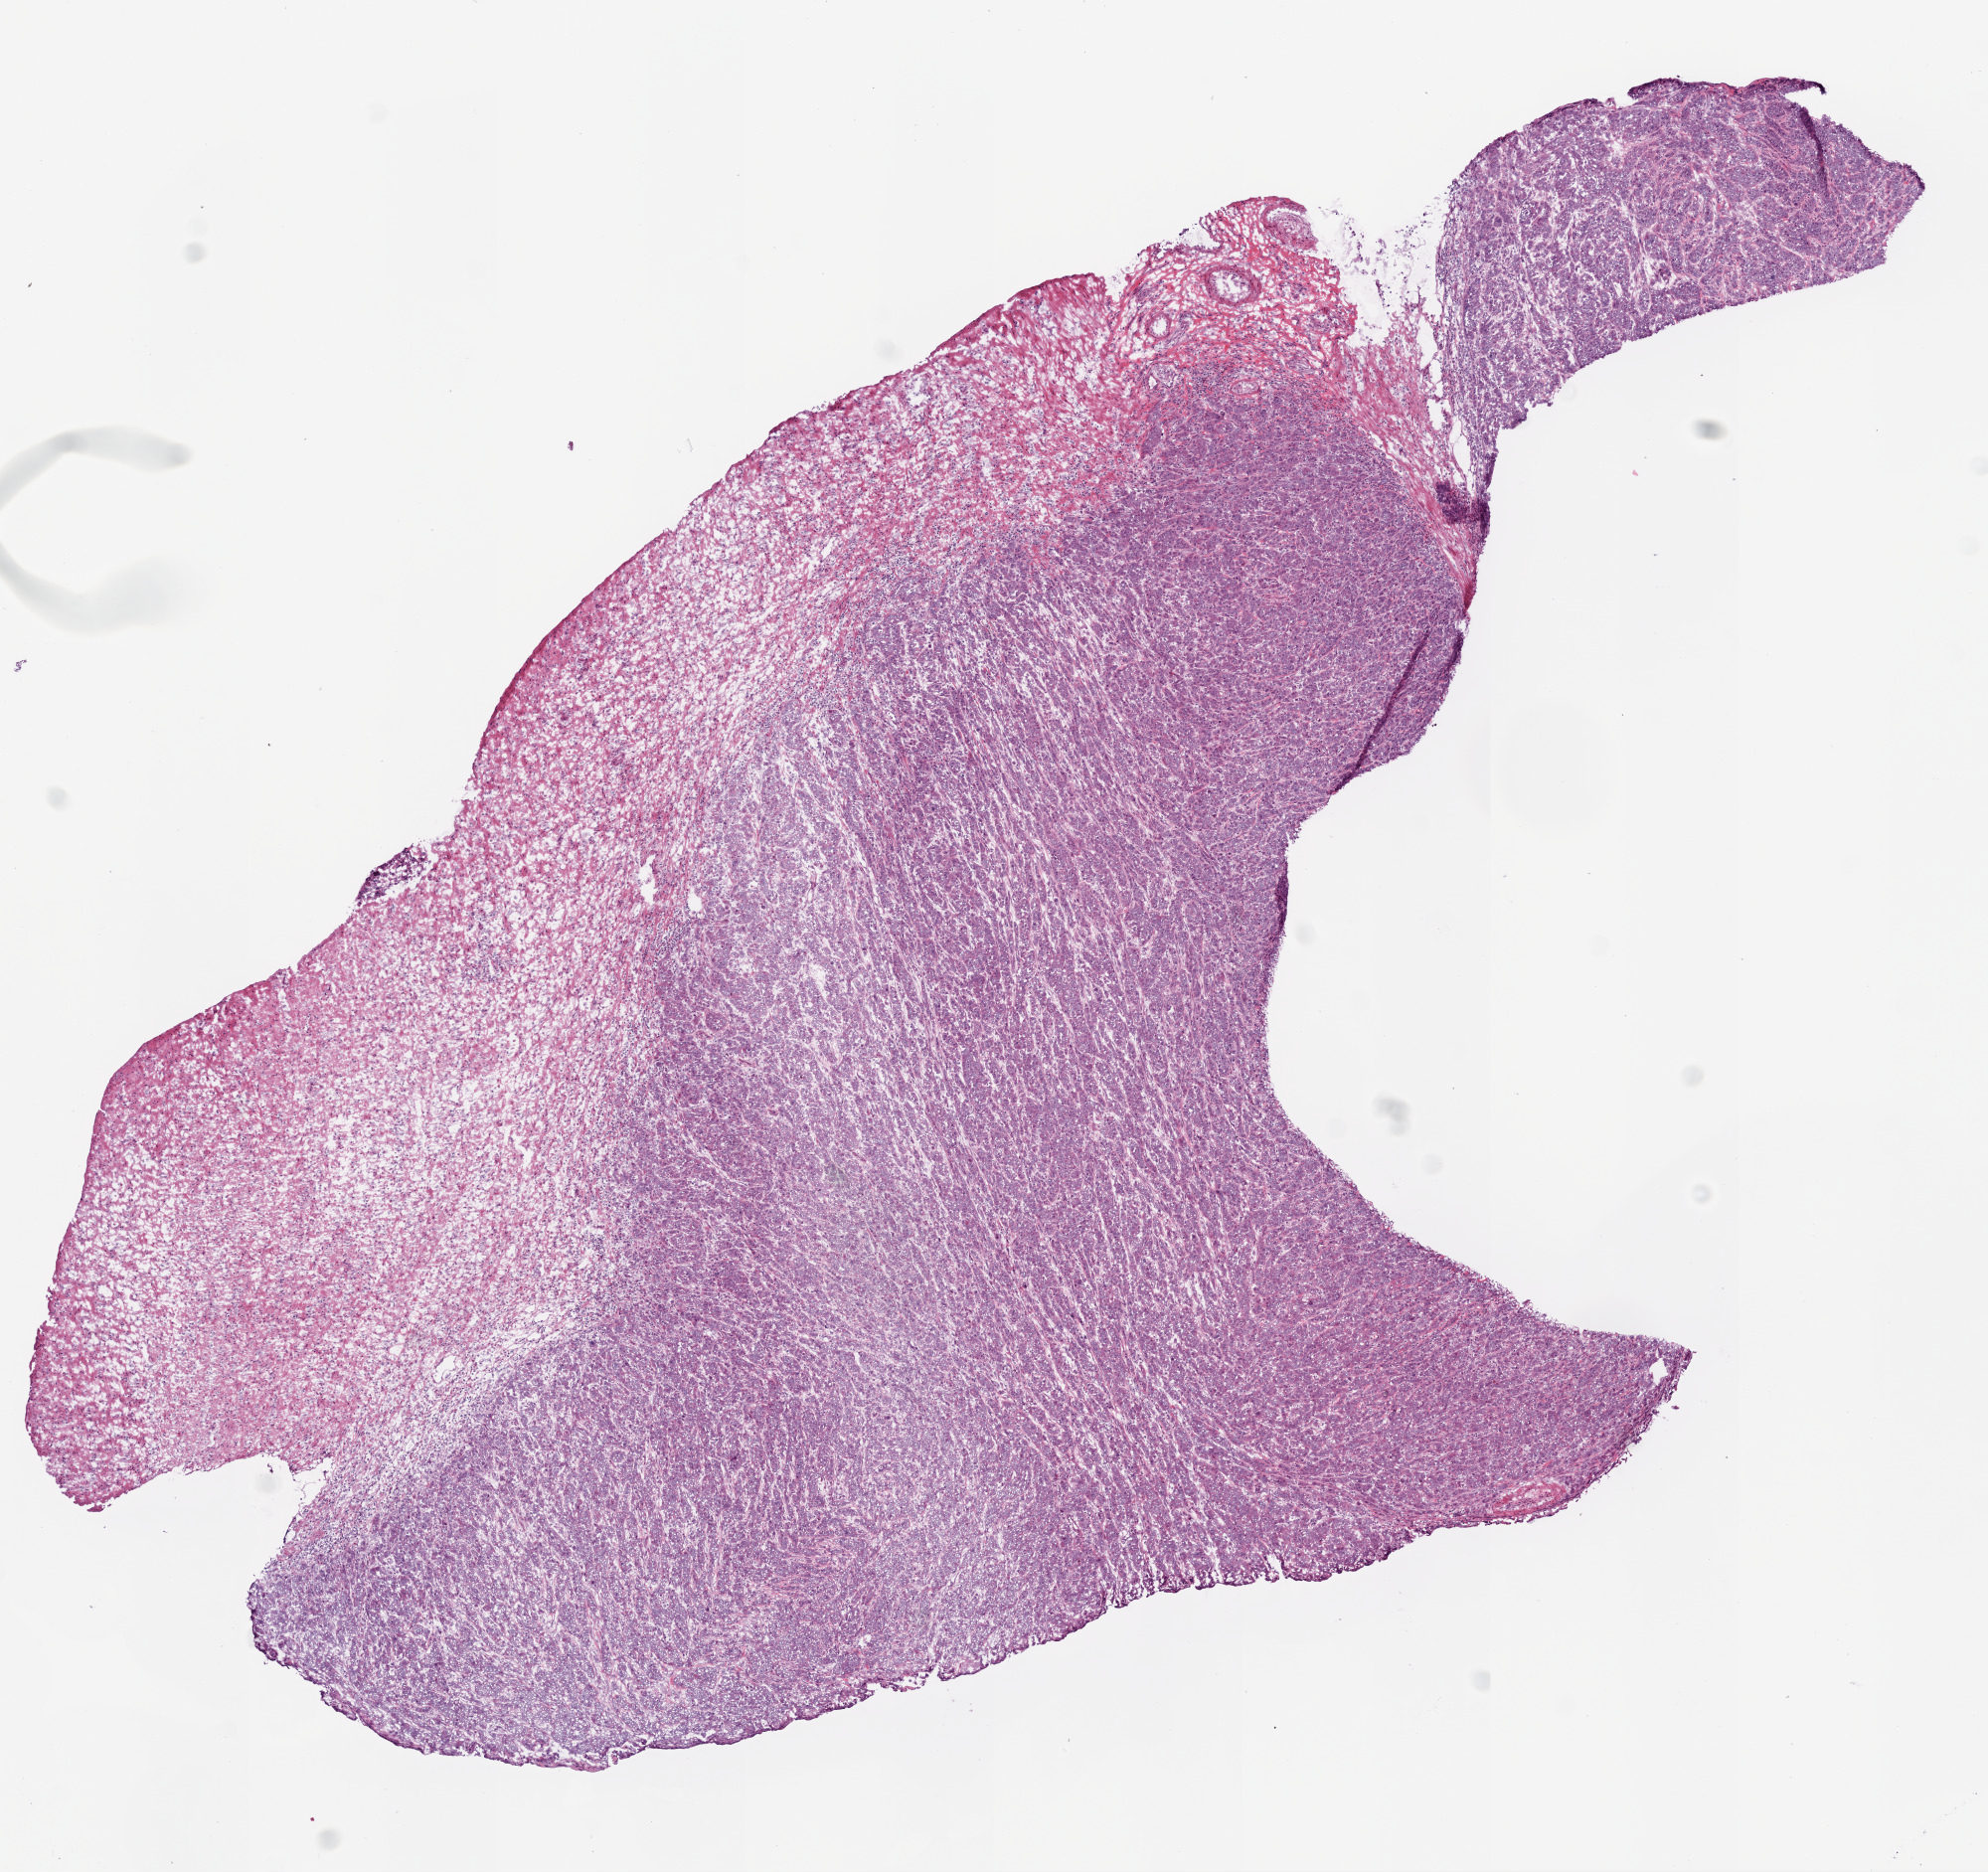
Whole-slide histology image, H&E — shown as a low-resolution overview of the whole scanned area (about 8.0 x 7.6 mm, acquisition: 20x scan). Frozen section. Sample: primary tumour, rectum. Male patient; age at initial diagnosis 51 years. Composition of this section per pathologist review: tumour cells 74%, tumour nuclei 80%, normal cells 0%, stromal cells 25%, necrosis 1%.
* AJCC pathologic stage: II (5th edition)
* pathologic diagnosis: Adenocarcinoma, NOS